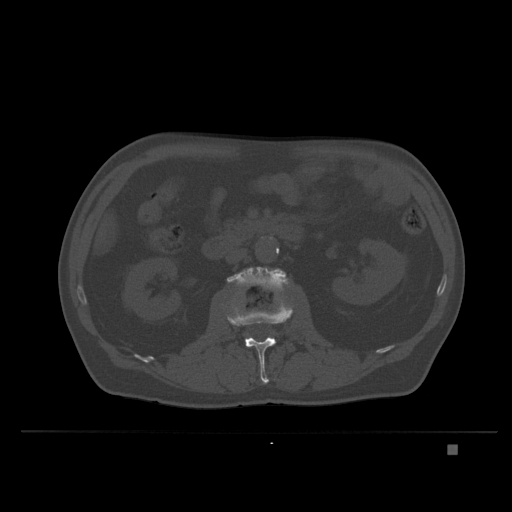
CT including the spine, one axial slice. Slice 112 of 435 in the series (ordered by position). Bone window (W 1800 / L 400 HU). 512 × 512 image matrix, field of view 434 × 434 mm. Male patient, age 73 years. Case-level facts recorded for this patient, not image findings: primary cancer: skin.
Outlined on this slice (semi-automatic segmentation, software-assisted and operator-edited):
- L2 vertebra: bounding box <226,296,294,384> (left, top, right, bottom; pixels)
- L3 vertebra: <227,267,289,288>